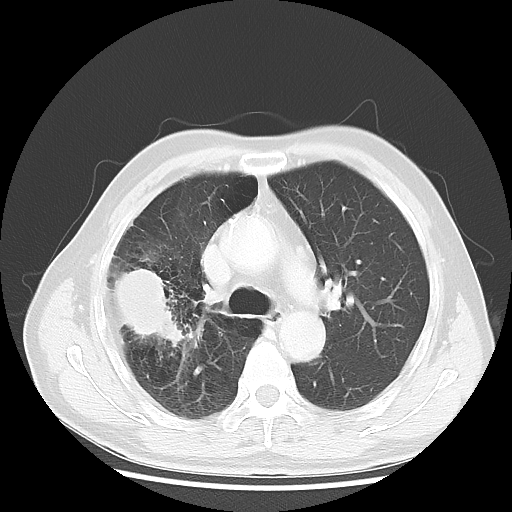
Chest CT, one axial slice. Position 32 of 50 along the scan axis. 120 kVp. Lung window (W 1500 / L -600 HU). 512 × 512 image matrix. Patient: male, 69 years. From the clinical record (not read from this slice): clinical TNM (as recorded): T3 N0 M0; histopathological grade: G3.
Outlined on this slice (bounding box drawn by a radiologist):
- lung tumour (recorded histology: adenocarcinoma): box from (x=112, y=261) to (x=187, y=349) px